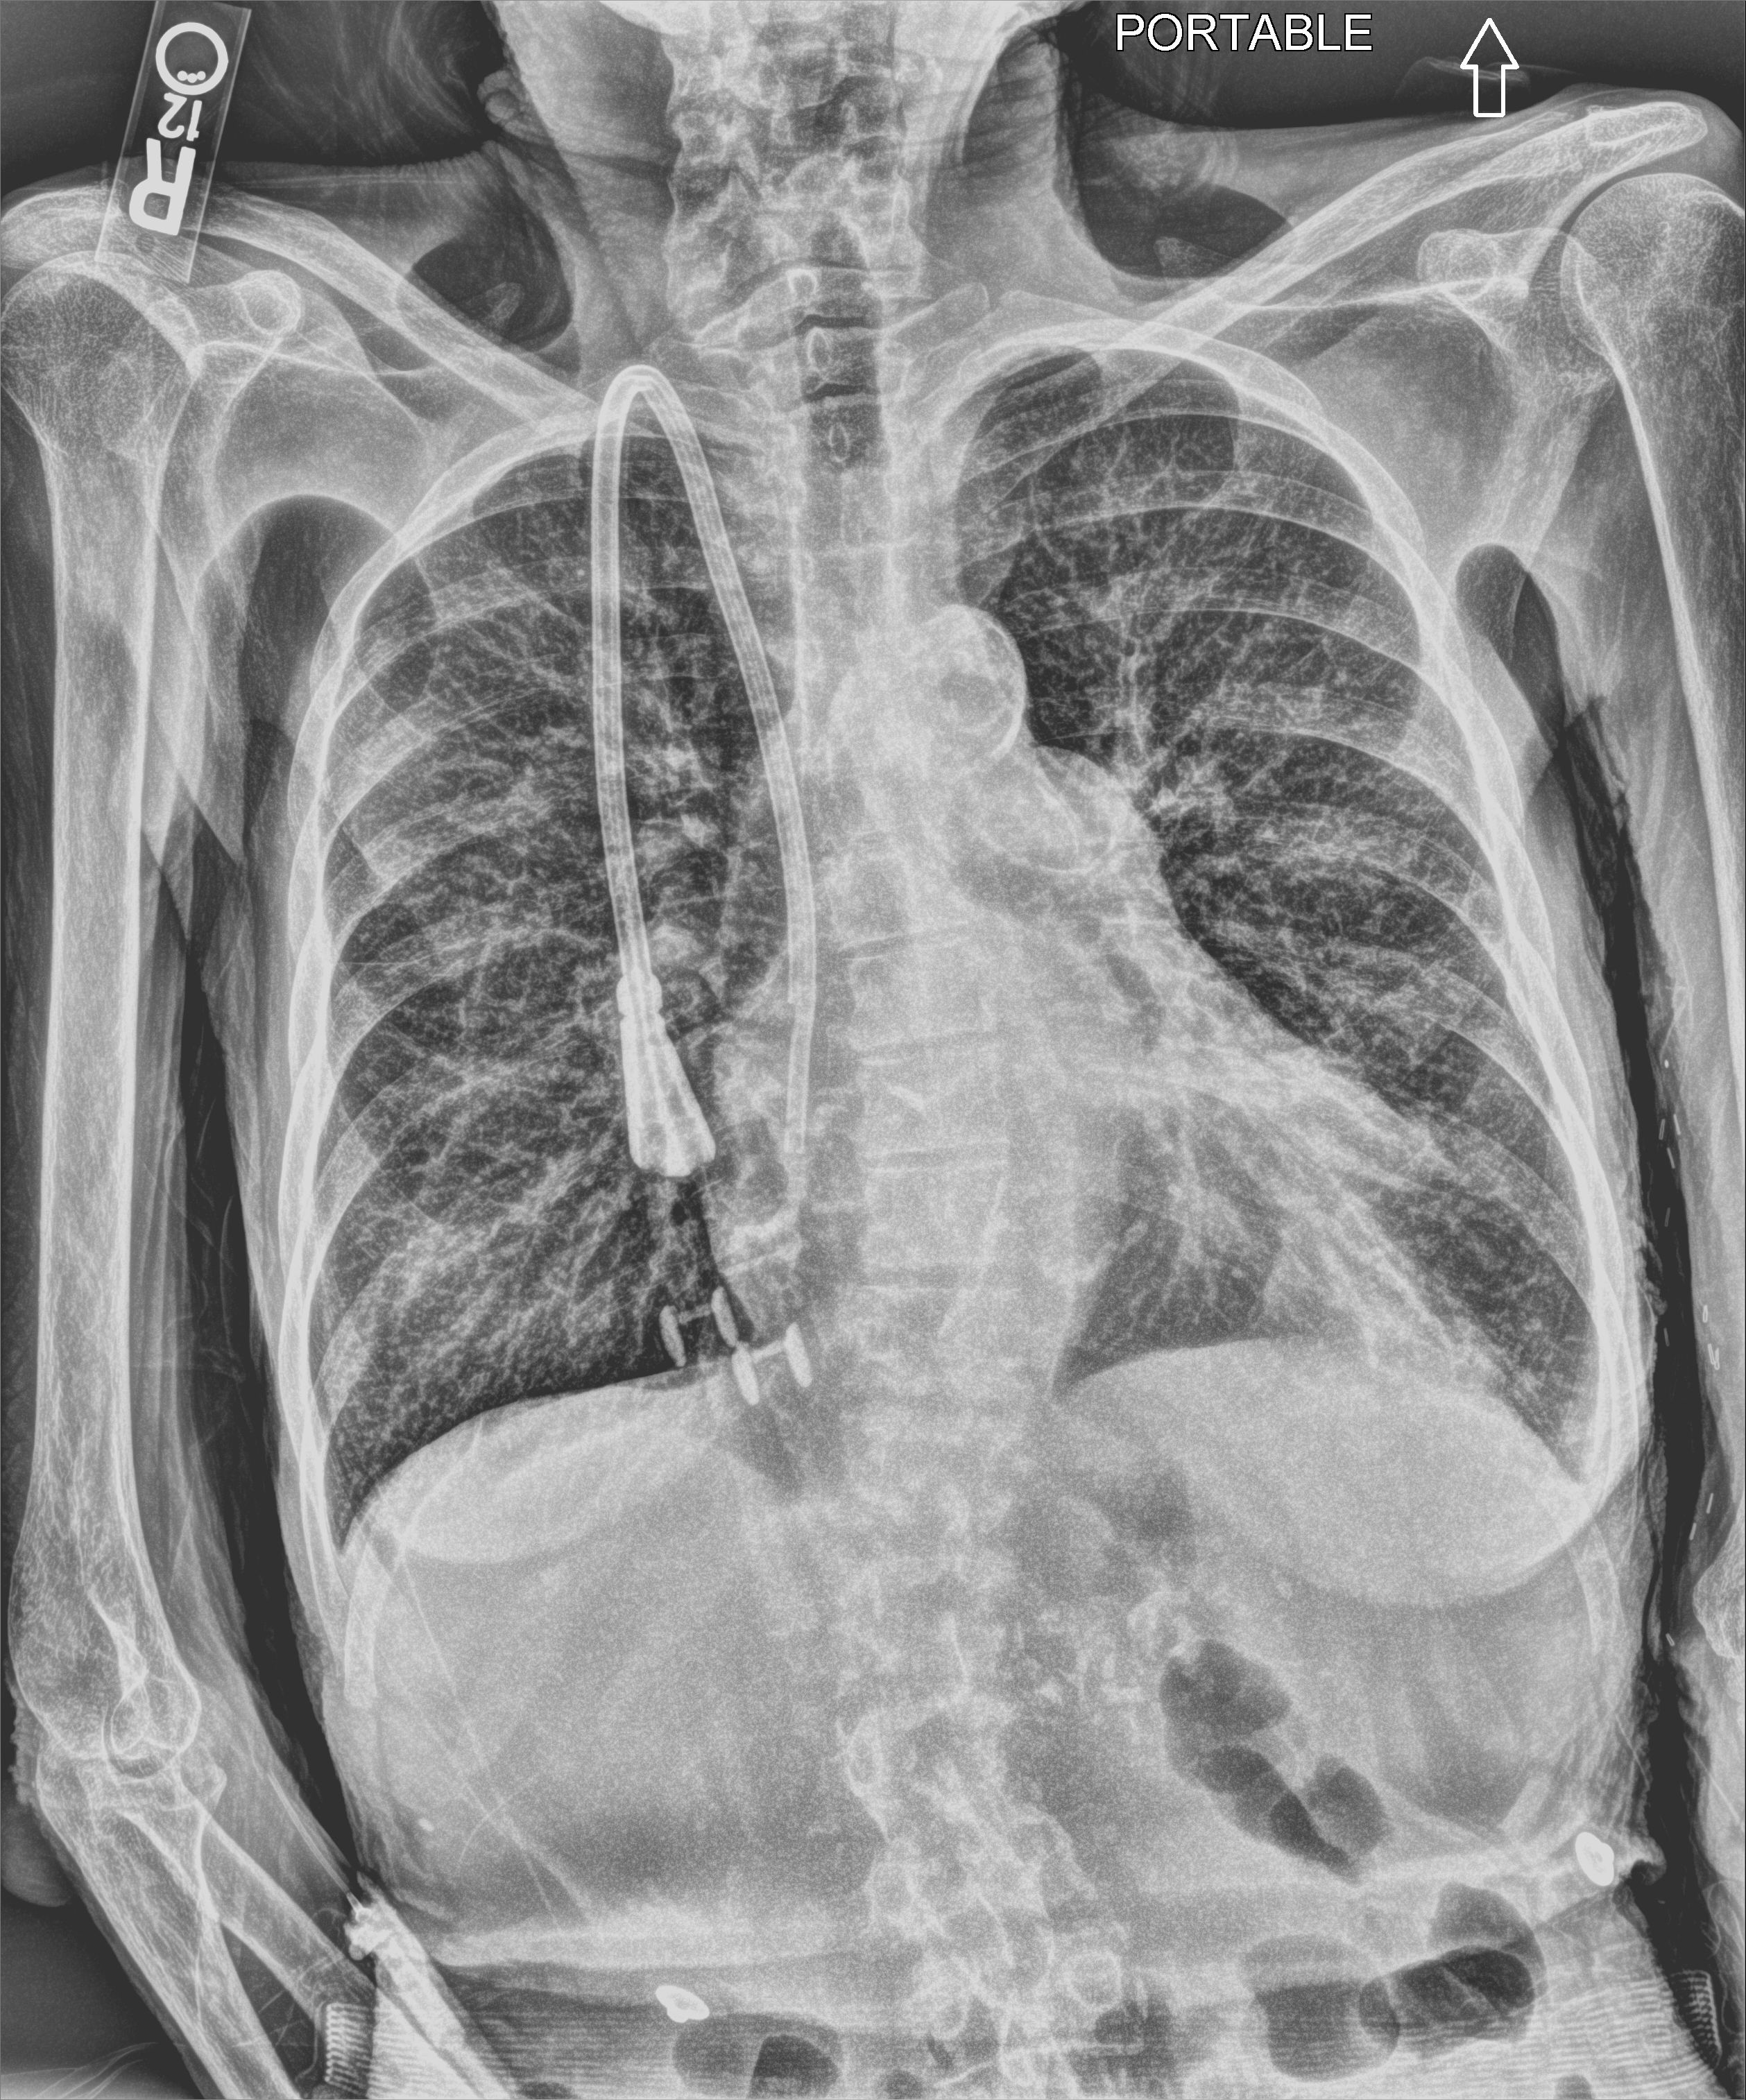
Chest X-ray (portable); anteroposterior (AP) projection. Female patient hospitalised with COVID-19, age 60–74 years.
Hospital-stay facts (about this admission, not read from this image; timing relative to this image not recorded): other chronic lung disease (admission record): no; mechanically ventilated during this hospital stay: no.